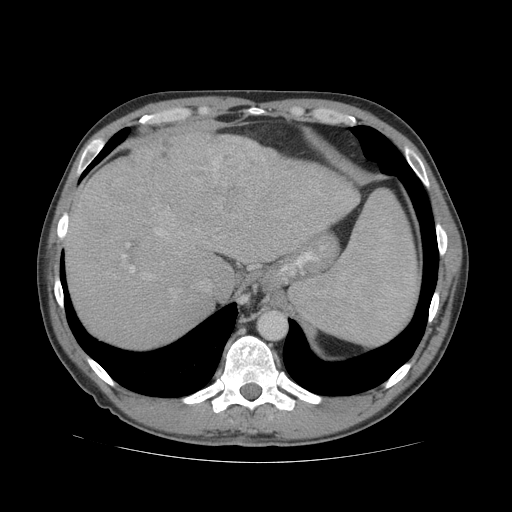
Contrast-enhanced abdominal CT (liver protocol), one axial slice. Reconstruction kernel STANDARD. 140 kVp. Soft-tissue window (W 400 / L 40 HU). 2.5 mm slice thickness. 512 × 512 image matrix. Case-level facts recorded for this patient, not image findings: diagnosis: hepatocellular carcinoma (patient treated with transarterial chemoembolisation; whether this scan precedes or follows treatment is not stated here); TNM stage (as recorded): Stage-IVB.
Structures marked on this image (semi-automatic segmentation, software-assisted and operator-edited):
- abdominal aorta: bounding box <259,313,286,339> (left, top, right, bottom; pixels)
- liver parenchyma outside the tumour (the mass and vessels are separate outlines, so this box may not span the whole liver): <66,134,359,348>
- mass: <79,133,271,233>
- liver vessels: <121,229,168,276>